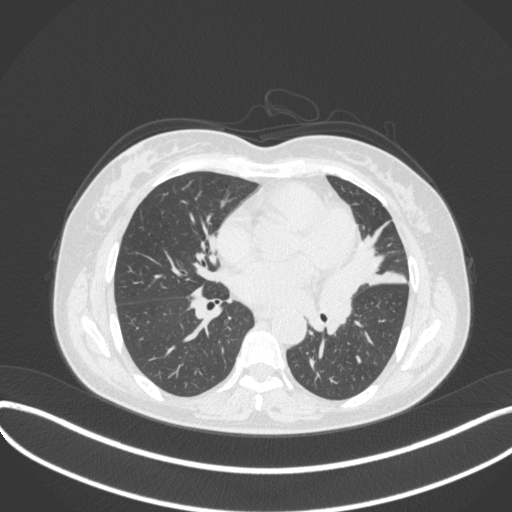
Chest CT, one axial slice; position 169 of 373 along the scan axis; reconstruction kernel B31f; 120 kVp; lung window (W 1500 / L -600 HU); 1 mm slice thickness; 512 × 512 image matrix, field of view 400 × 400 mm. Patient: female, 54 years. Case-level facts recorded for this patient, not image findings: clinical TNM (as recorded): T2a N1 M0.
Outlined on this slice (rectangle marked by the reading radiologist):
- lung tumour (recorded histology: small cell carcinoma): bounding box (x1, y1, x2, y2) in pixels: (315, 265, 361, 333)